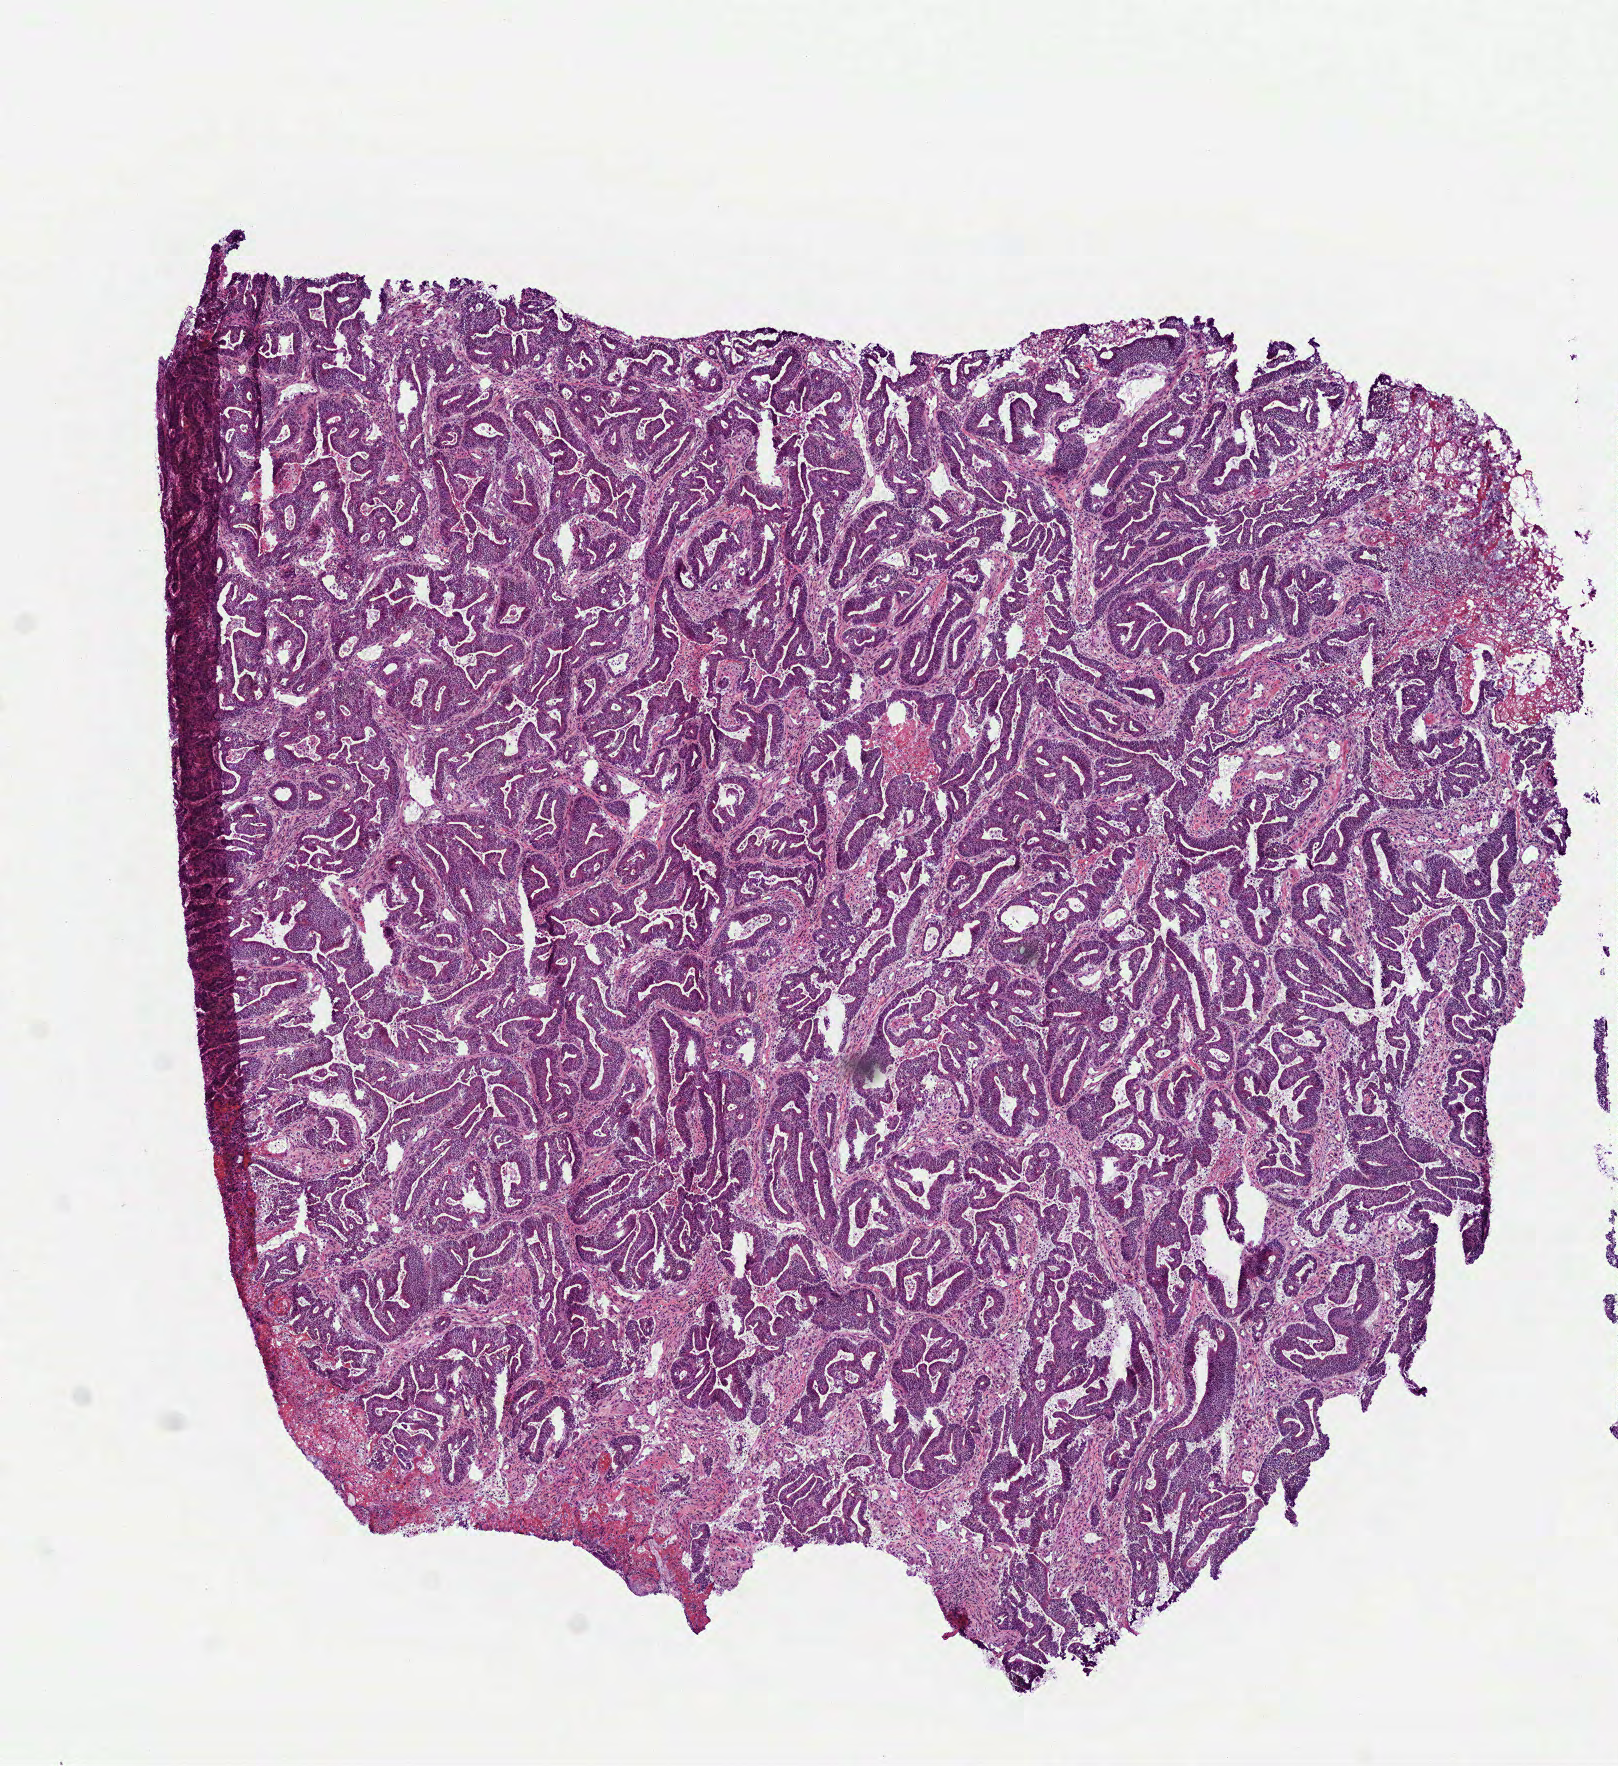
Hematoxylin and eosin (H&E) stained whole-slide image — a low-resolution overview of the entire scanned area, about 6.5 x 7.1 mm (from a 40x scan), frozen section from the bottom of the tissue portion, primary tumour sample from the stomach. Male patient. Histologic grade: G2 (moderately differentiated). Slide review estimates, as recorded: tumour cells 88%, tumour nuclei 80%, normal cells 0%, stromal cells 12%, necrosis 0%.
Lymph nodes positive (case pathology): 2 of 7 examined. AJCC pathologic stage: I (6th edition). Pathologic diagnosis: Adenocarcinoma, NOS.